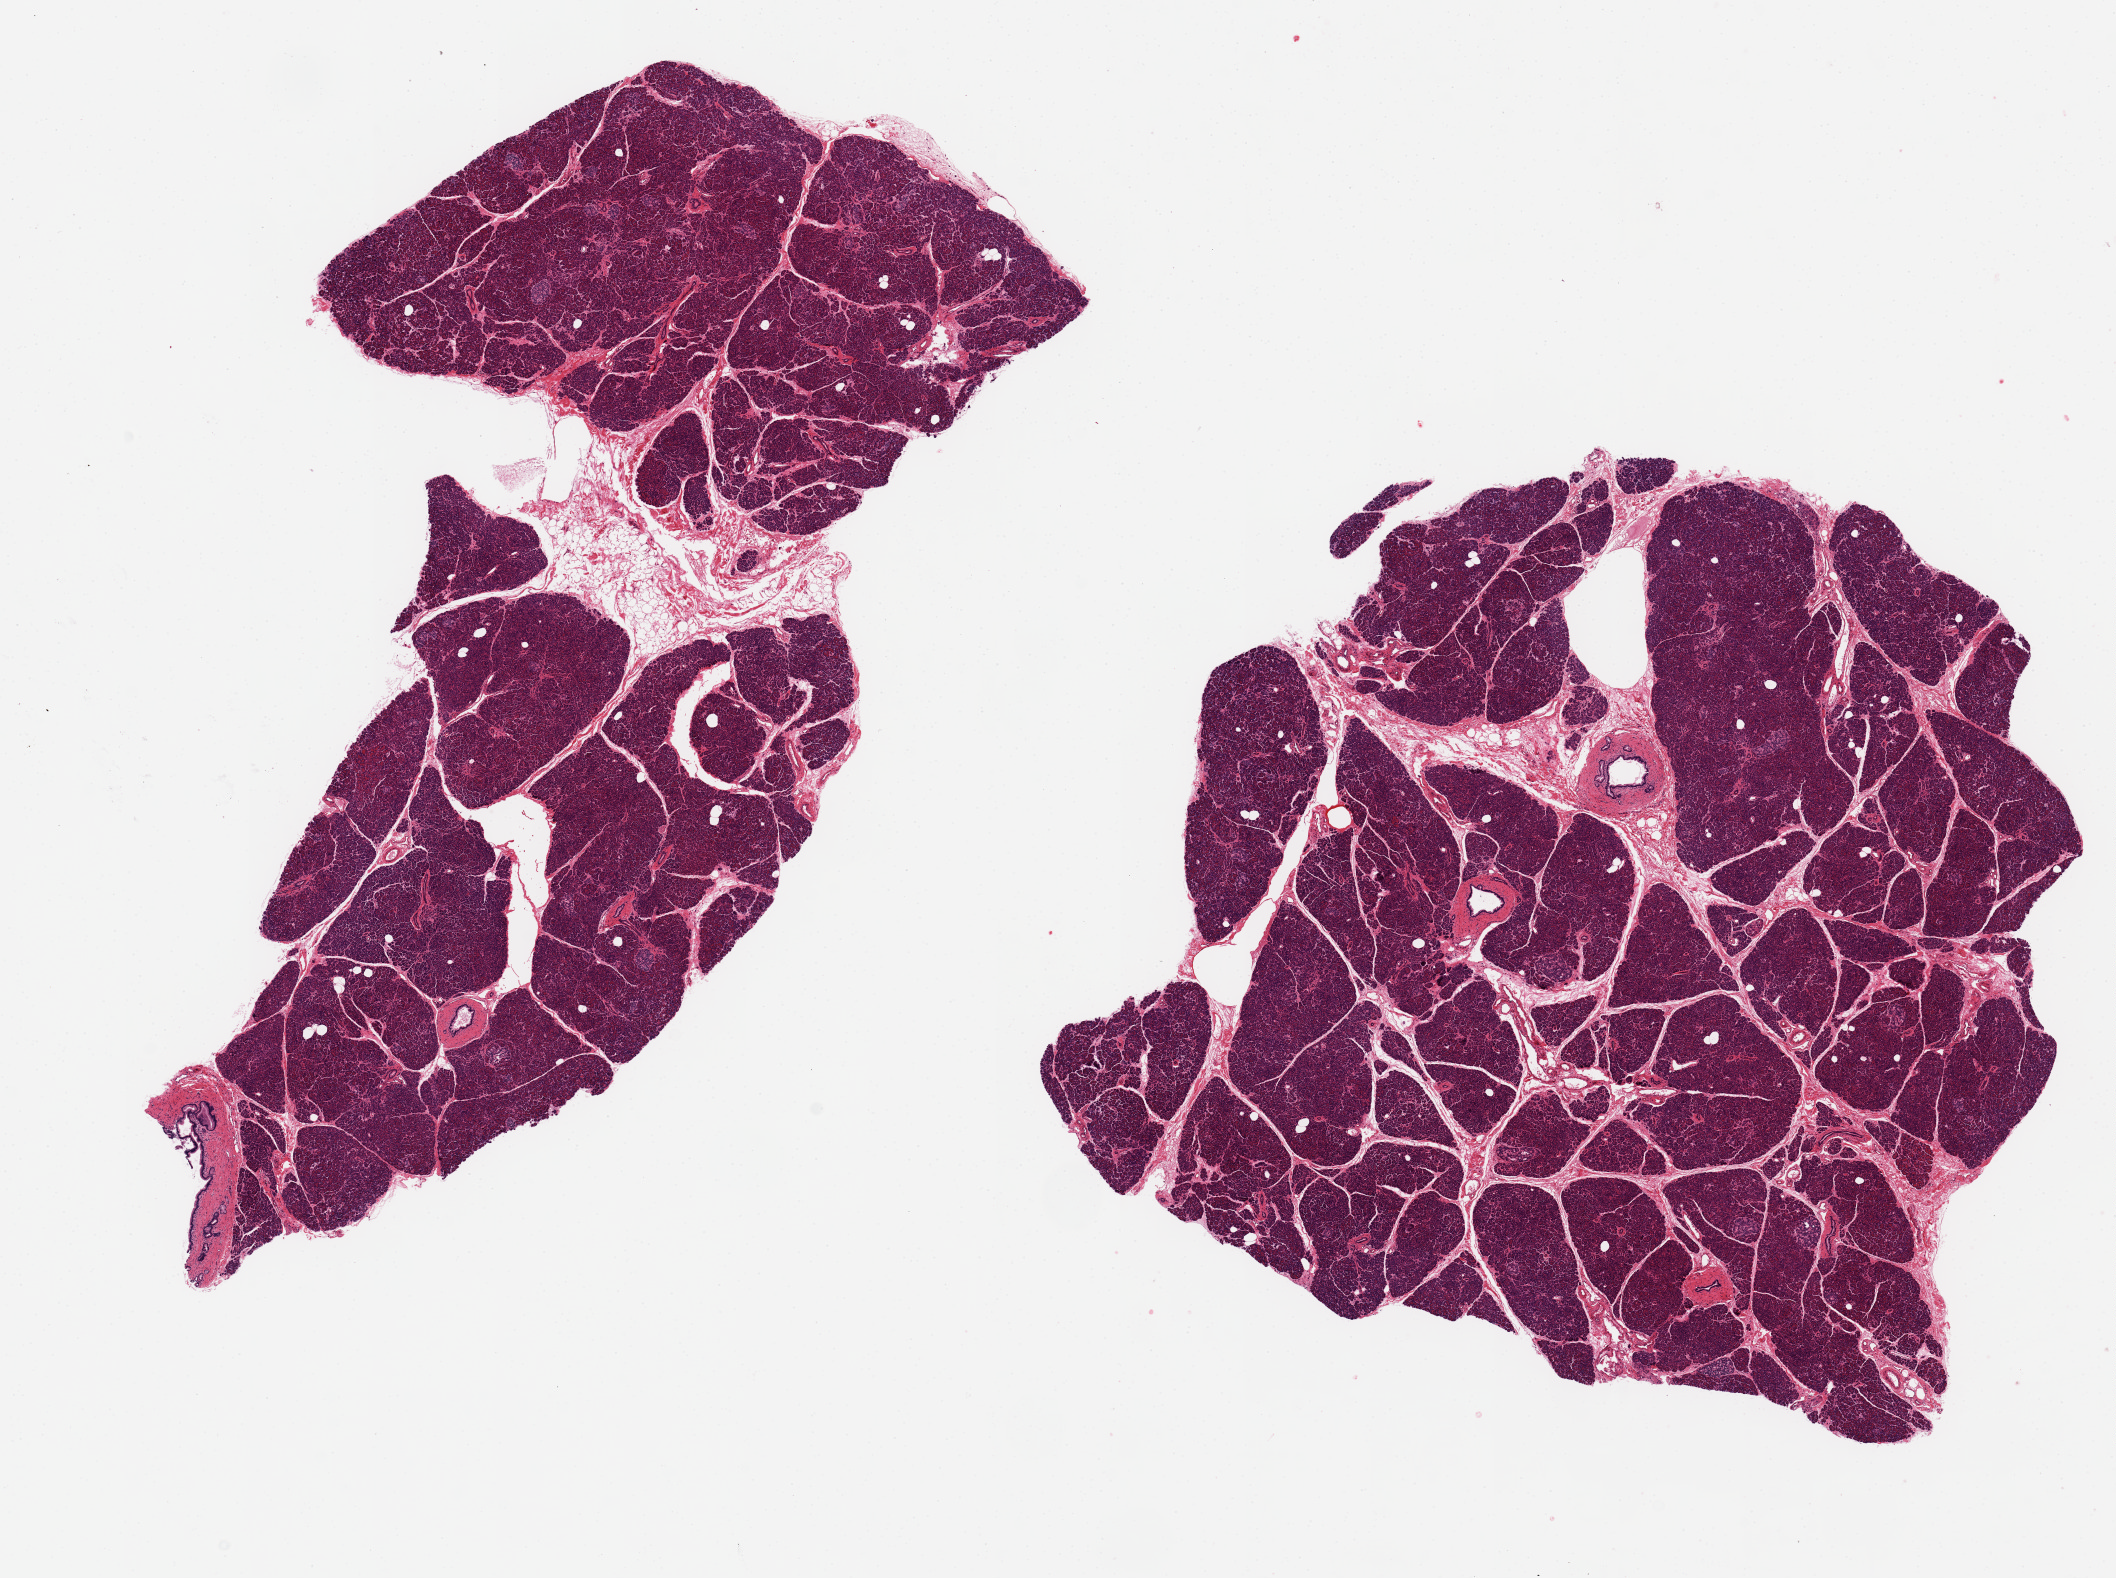
Digitized H&E-stained section, low-resolution overview of the scanned area, about 16.7 x 12.5 mm (from a 20x scan). PAXgene-fixed, paraffin-embedded tissue. Section of pancreas (target tissue). Donor tissue sample. Female donor.
Review note (as recorded): 2 pieces, 7x7 & 10x4 mm; very good exo and endocrine glands and ducts; <5% fat.